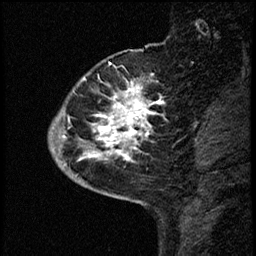
Breast MRI (dynamic contrast-enhanced), one sagittal slice; slice 13 of 68 in the series (ordered by position); dynamic contrast-enhanced study with each time point stored as its own series, time point 2 of 3 at this slice position (early post-contrast, ordered by acquisition time); 1.5 T; TE 4.2 ms, TR 17.6 ms; 2 mm slice thickness; 256 × 256 image matrix. Patient: female, 52 years. Case-level facts recorded for this patient, not image findings: setting: breast cancer imaged before/during neoadjuvant chemotherapy; receptor status: HER2-positive.
Outlined on this slice (semi-automatic segmentation, software-assisted and operator-edited):
- analysis volume of interest (the breast-tissue region the enhancement analysis was run in; not a lesion): bounding box <50,61,174,184> (left, top, right, bottom; pixels)
- tumour enhancement mask (voxels above the 100 % enhancement threshold inside the analysis volume of interest): <58,81,160,167>